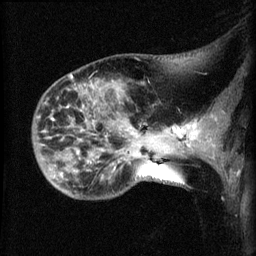
Breast MRI (dynamic contrast-enhanced), one sagittal slice. Slice 18 of 60 in the series (ordered by position). Dynamic contrast-enhanced series, image 2 of 3 at this slice position (ordered by acquisition). 1.5 T. TE 4.2 ms, TR 8.2 ms. 2.1 mm slice thickness. 256 × 256 image matrix, field of view 180 × 180 mm. Female patient, age 50 years.
Outlined on this slice (semi-automatically segmented with operator editing):
- analysis volume of interest (the breast-tissue region the enhancement analysis was run in; not a lesion): bounding box [x1, y1, x2, y2] px = [38, 77, 169, 199]
- tumour enhancement mask (voxels above the 70 % enhancement threshold inside the analysis volume of interest): [164, 128, 169, 132]